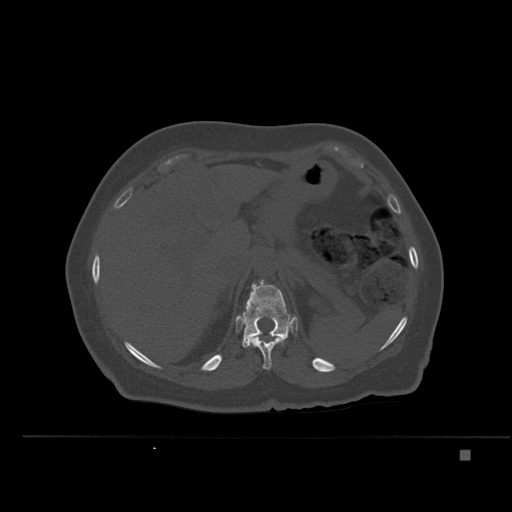
CT including the spine, one axial slice; slice 259 of 477 in the series (ordered by position); bone window (W 1800 / L 400 HU); 1.5 mm slice thickness; 512 × 512 image matrix, field of view 422 × 422 mm. Patient: female, 74 years. From the clinical record (not read from this slice): primary cancer: colon.
Outlined on this slice (semi-automatically segmented with operator editing):
- T11 vertebra: box from (x=250, y=336) to (x=283, y=370) px
- T12 vertebra: (x=242, y=280)–(x=293, y=347)